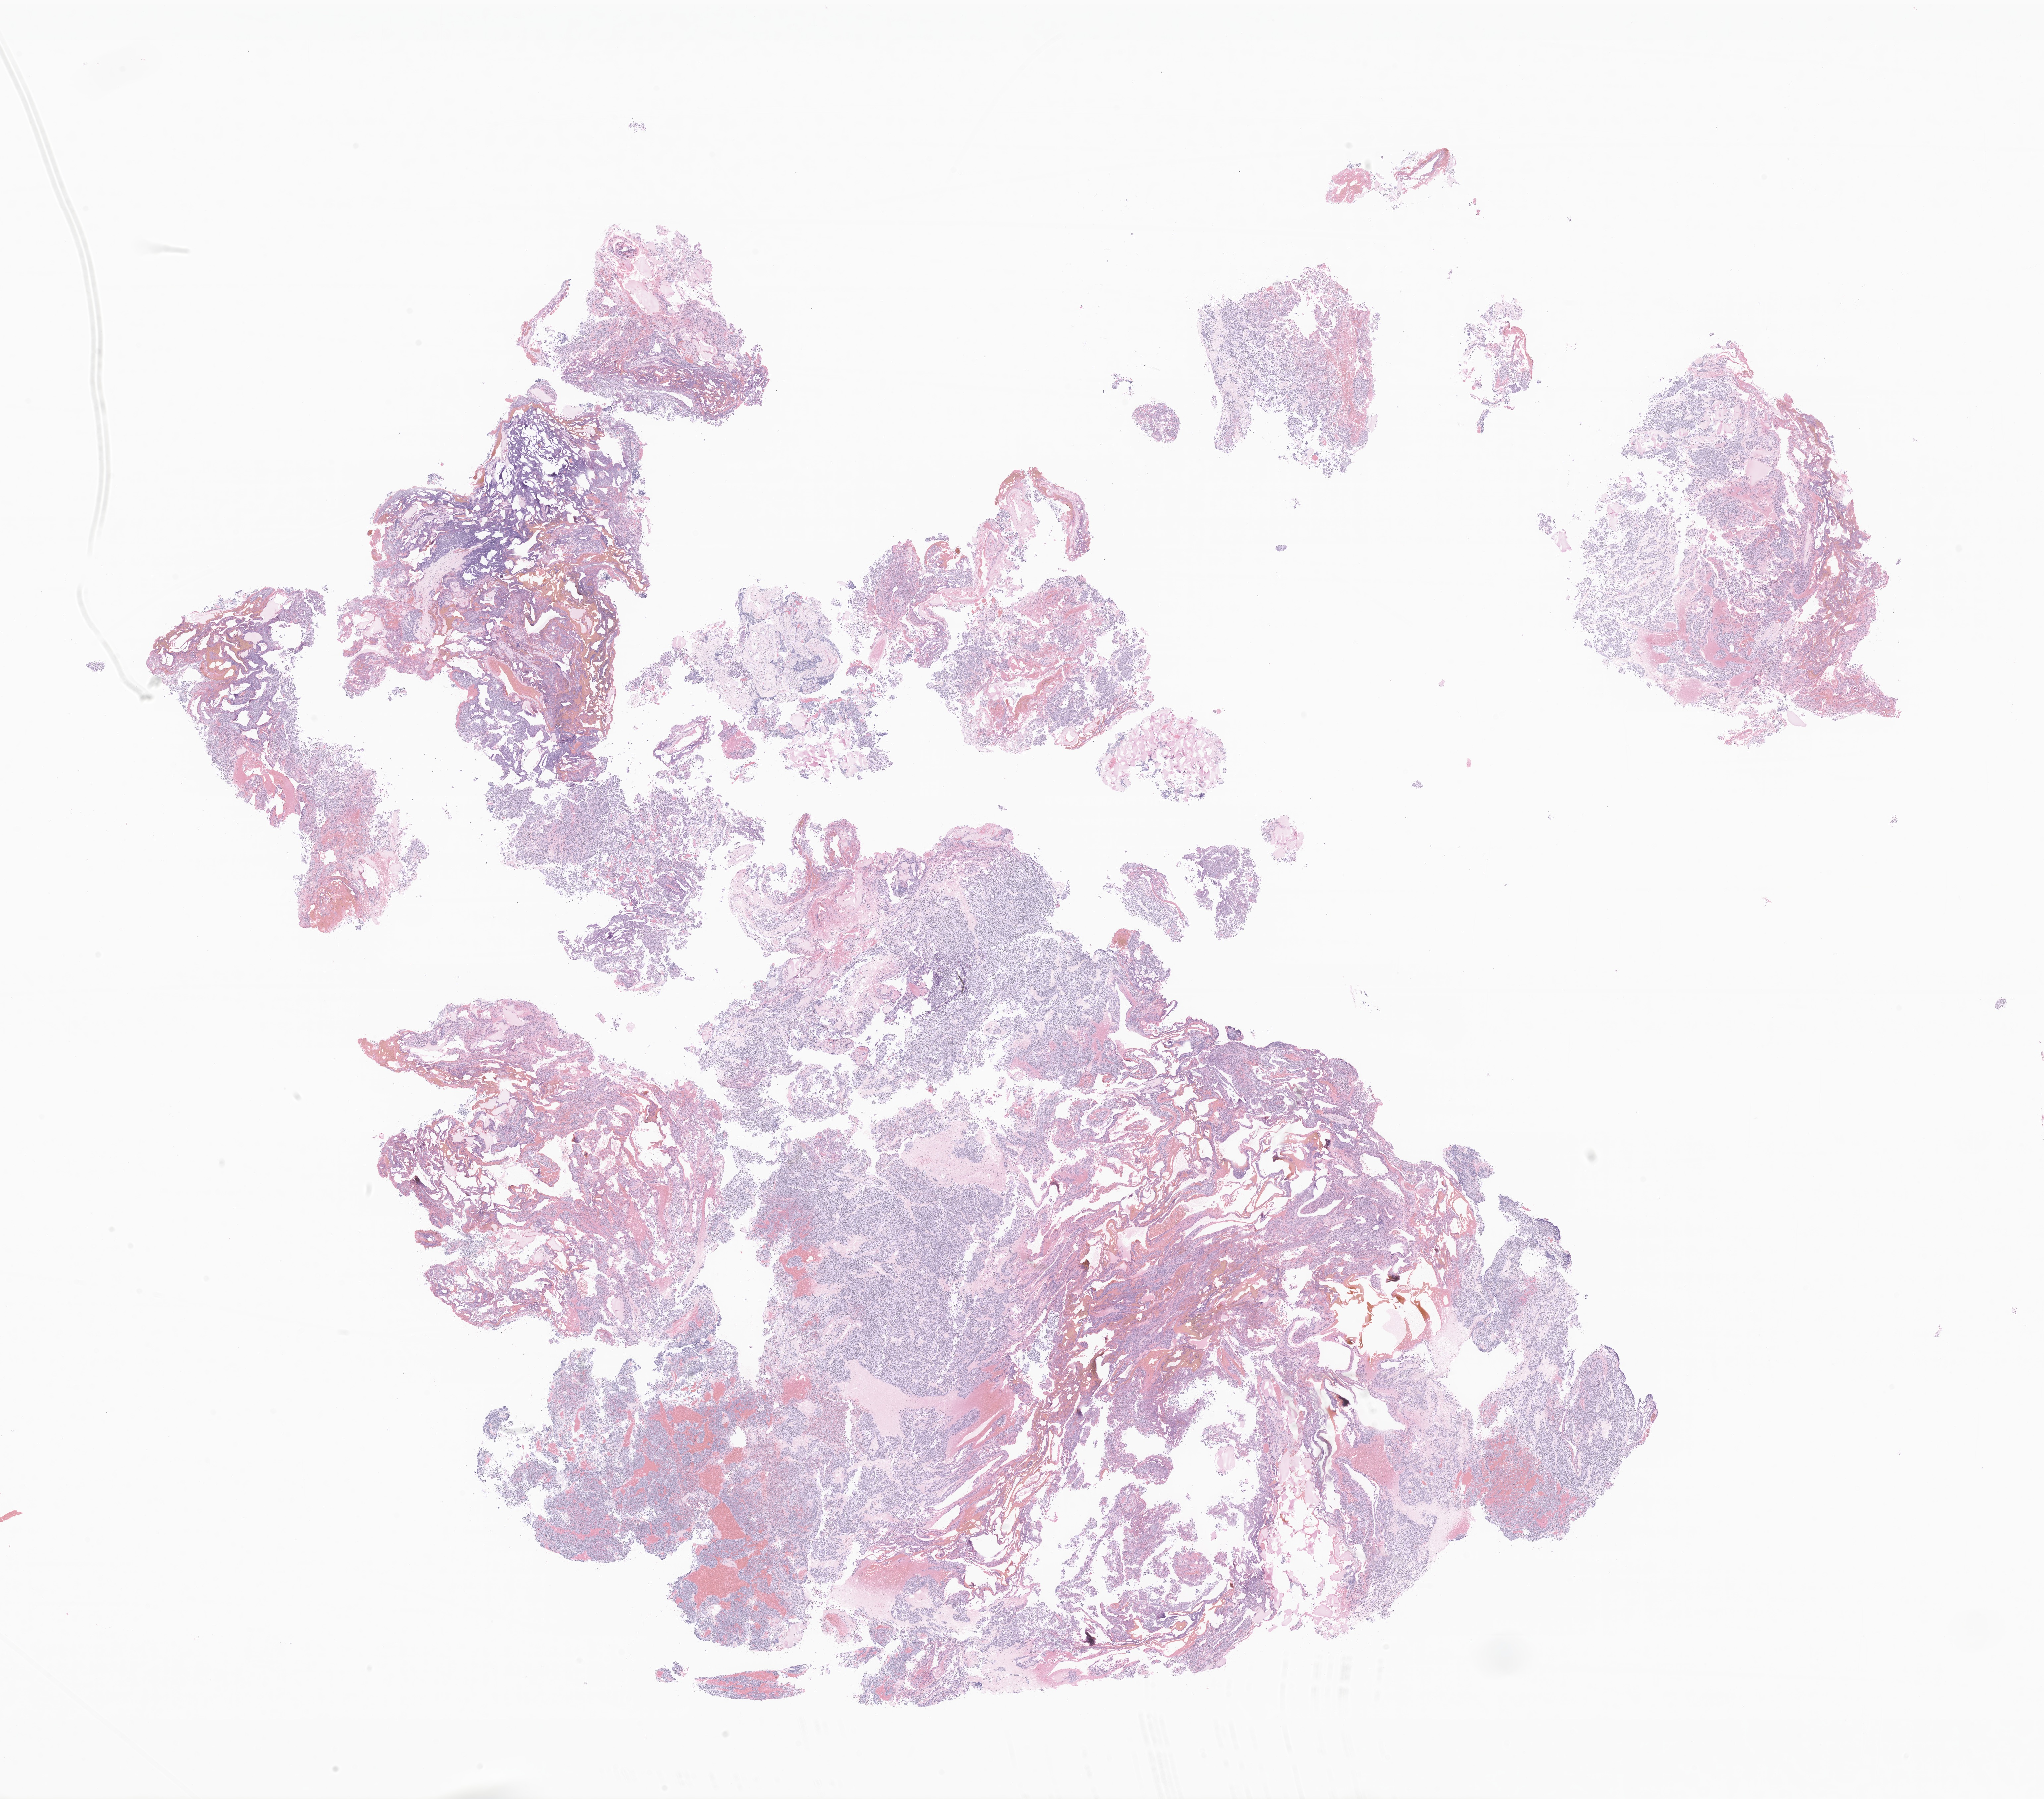
Whole-slide image, hematoxylin and eosin (H&E) stain of tumor tissue from the brain — a low-resolution overview of the entire scanned area, about 26.0 x 22.9 mm. Formalin-fixed paraffin-embedded section. Male patient, age 860 days (about 2.4 years).
- recorded diagnosis: Neoplasm, malignant, uncertain whether primary or metastatic